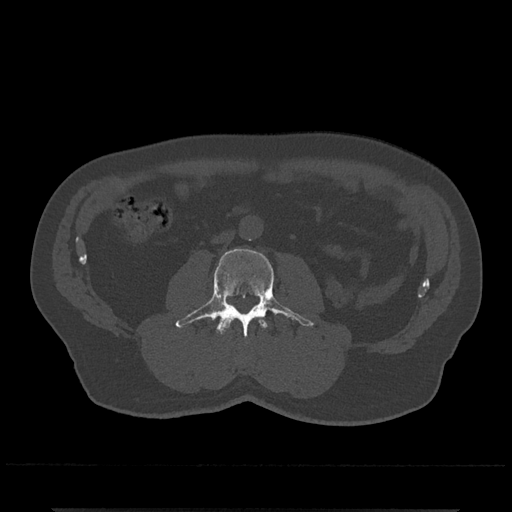
CT including the spine, one axial slice. Slice 227 of 797 in the series (ordered by position). Reconstruction kernel Br40s/3. 120 kVp. Bone window (W 1800 / L 400 HU). 512 × 512 image matrix, field of view 393 × 393 mm. Patient: male, 67 years. From the clinical record (not read from this slice): primary cancer: prostate.
Structures marked on this image (semi-automatic segmentation, software-assisted and operator-edited):
- L2 vertebra: bounding box <218,318,267,334> (left, top, right, bottom; pixels)
- L3 vertebra: <175,248,313,338>